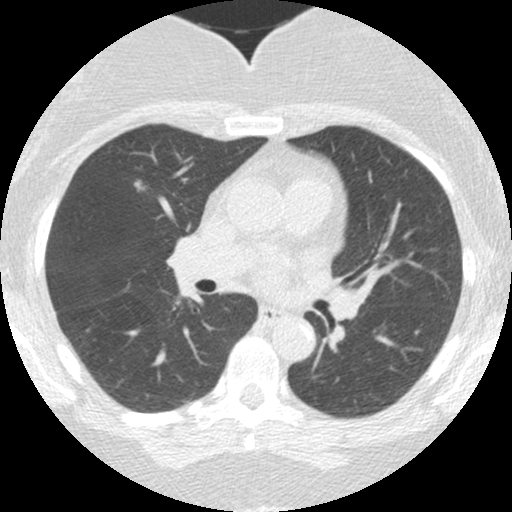
Low-dose screening chest CT, one axial slice; 120 kVp; lung window (W 1500 / L -600 HU); 2.5 mm slice thickness; 512 × 512 image matrix, field of view 286 × 286 mm.
Outlined on this slice (outlined manually by an expert reader):
- lesion 1 (tumor, upper lobe of right lung): box from (x=134, y=180) to (x=146, y=192) px